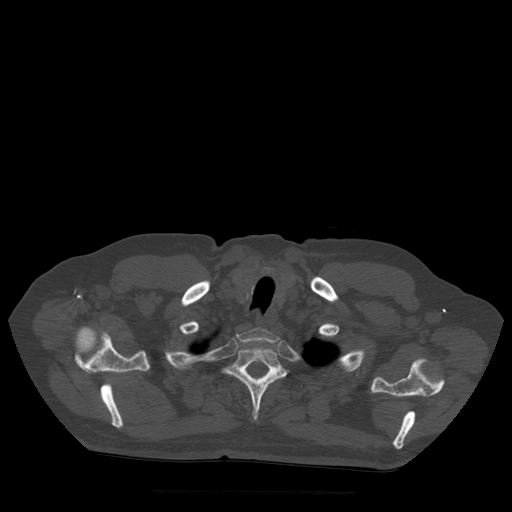
CT including the spine, one axial slice. Slice 426 of 522 in the series (ordered by position). Bone window (W 1800 / L 400 HU). 512 × 512 image matrix, field of view 420 × 420 mm. Patient age 72 years. Case-level facts recorded for this patient, not image findings: primary cancer: prostate.
Annotated regions visible in this slice (semi-automatic segmentation, software-assisted and operator-edited):
- T1 vertebra: bounding box <237,329,280,344> (left, top, right, bottom; pixels)
- T2 vertebra: <224,347,287,420>